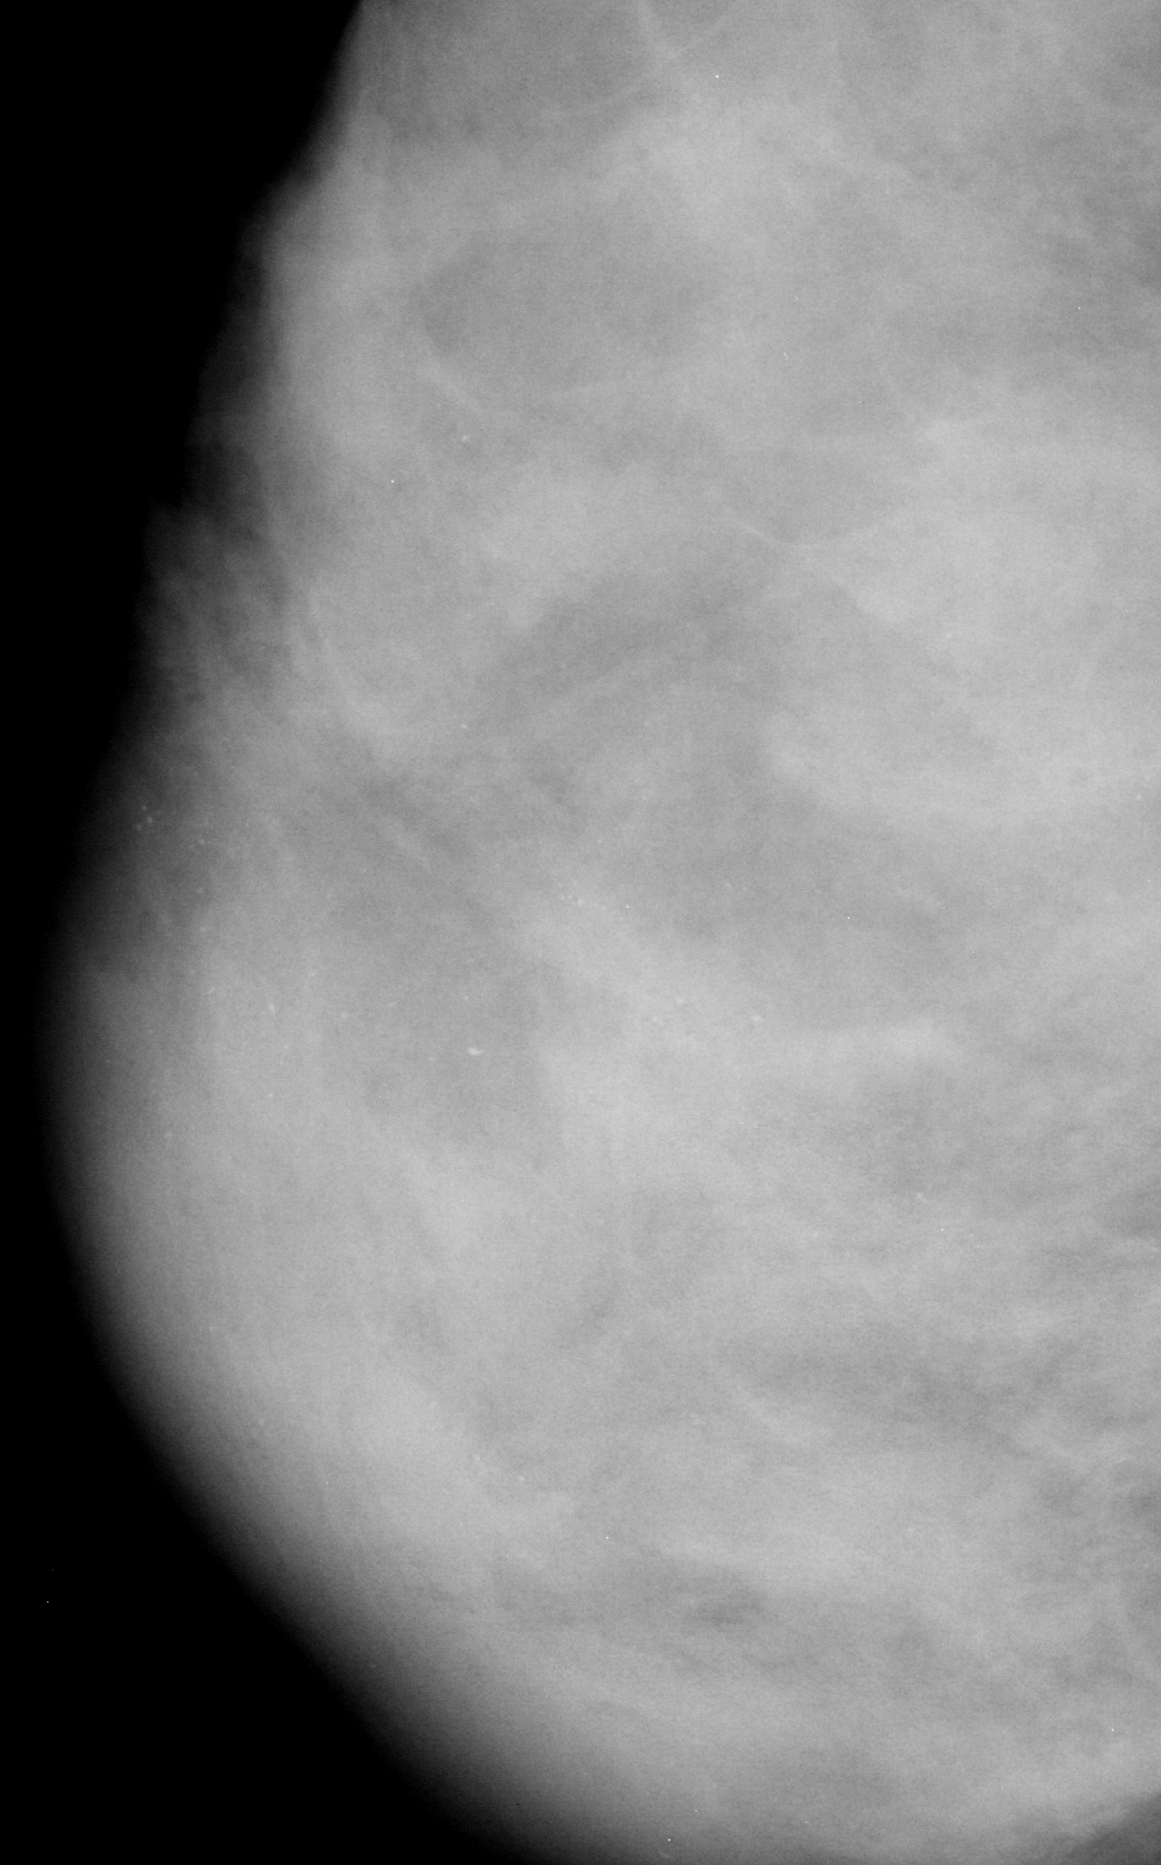
Cropped region of a digitized screen-film mammogram centred on a radiologist-marked abnormality; right breast; MLO view.
Finding: calcifications, morphology pleomorphic, distribution regional; BI-RADS assessment category 4; subtlety rating 3 on a 1 (subtle) to 5 (obvious) scale; pathology (as recorded): benign.